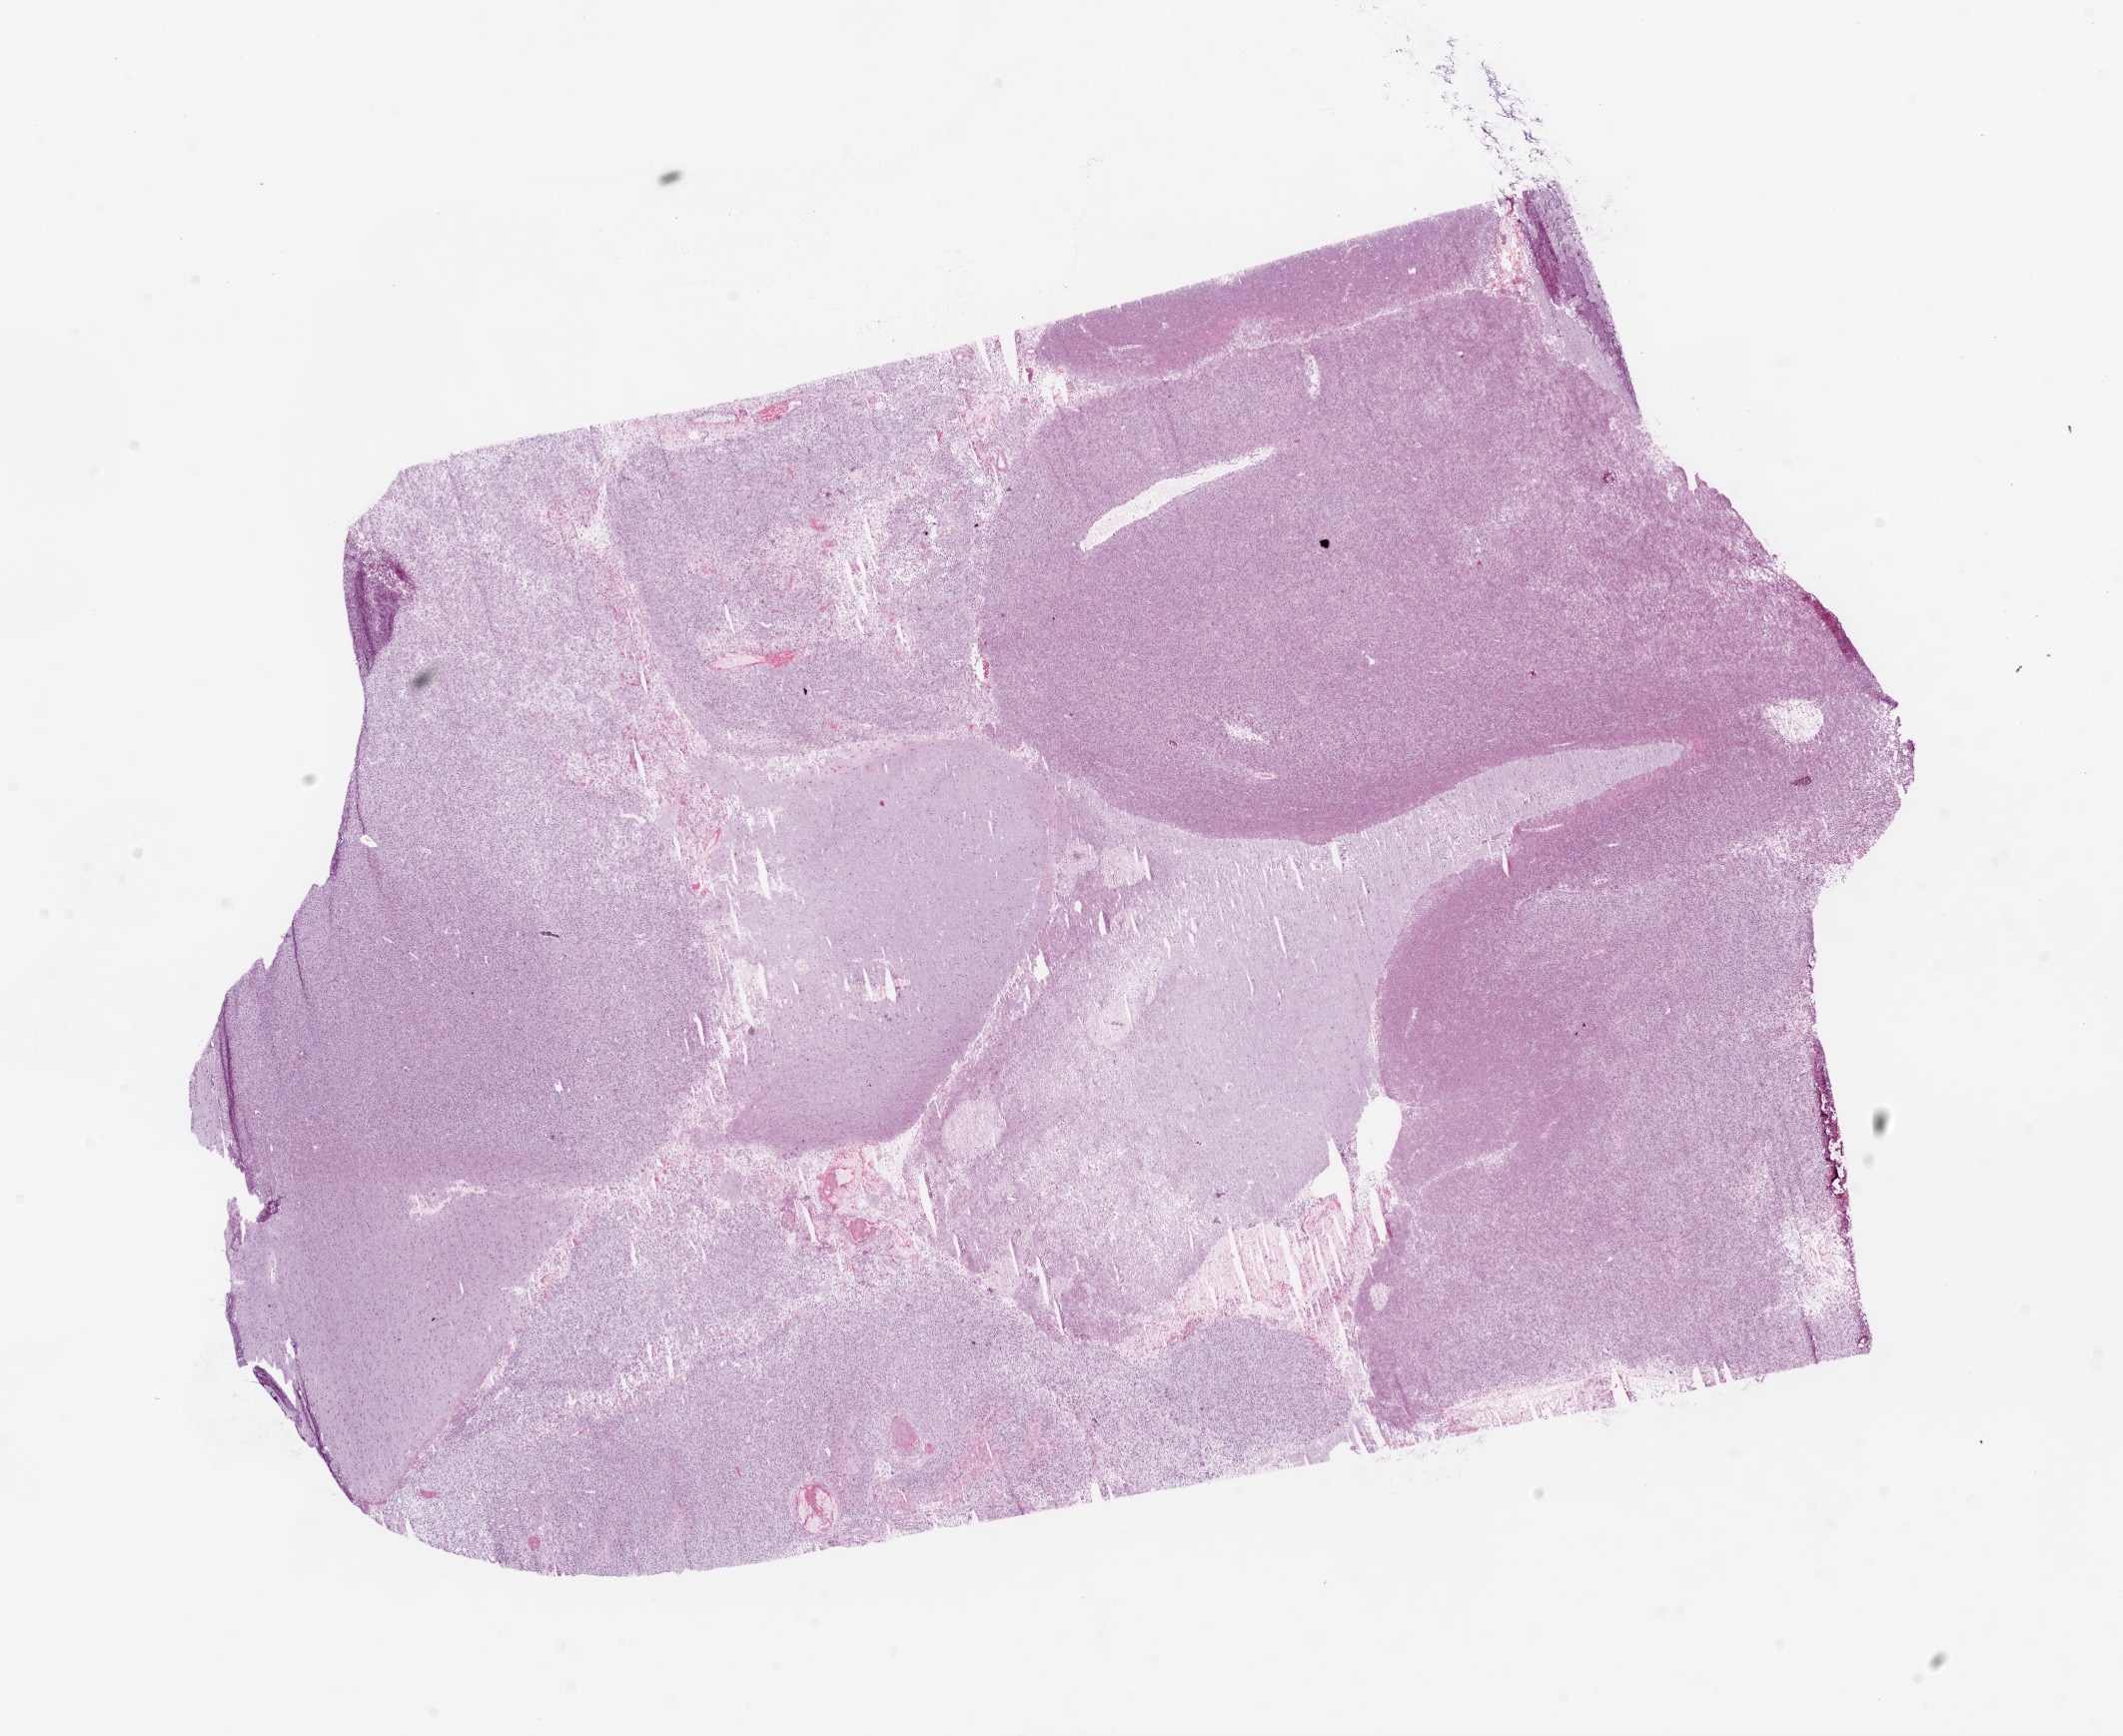
Digitized H&E tissue section (whole slide) — shown as a low-resolution overview of the whole scanned area (about 17.1 x 13.9 mm, slide scanned at 20x); frozen section; sample: primary tumour, brain. Patient: male, age at initial diagnosis 50 years. Pathologist review of this section (percent, as recorded): tumour cells 98%, tumour nuclei 80%, normal cells 0%, stromal cells 0%, necrosis 2%.
- diagnosis: Glioblastoma